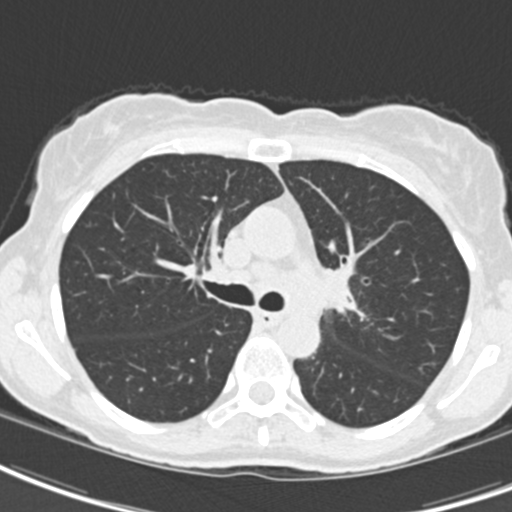
Low-dose screening chest CT, one axial slice. Slice 130 of 189 in the series (ordered by position). Reconstruction kernel B30f. Lung window (W 1500 / L -600 HU). 2 mm slice thickness. 512 × 512 image matrix, field of view 279 × 279 mm.
Structures marked on this image (manually delineated by an expert):
- lesion 2 (tumor, hilum of left lung): bounding box [x1, y1, x2, y2] px = [322, 266, 350, 311]